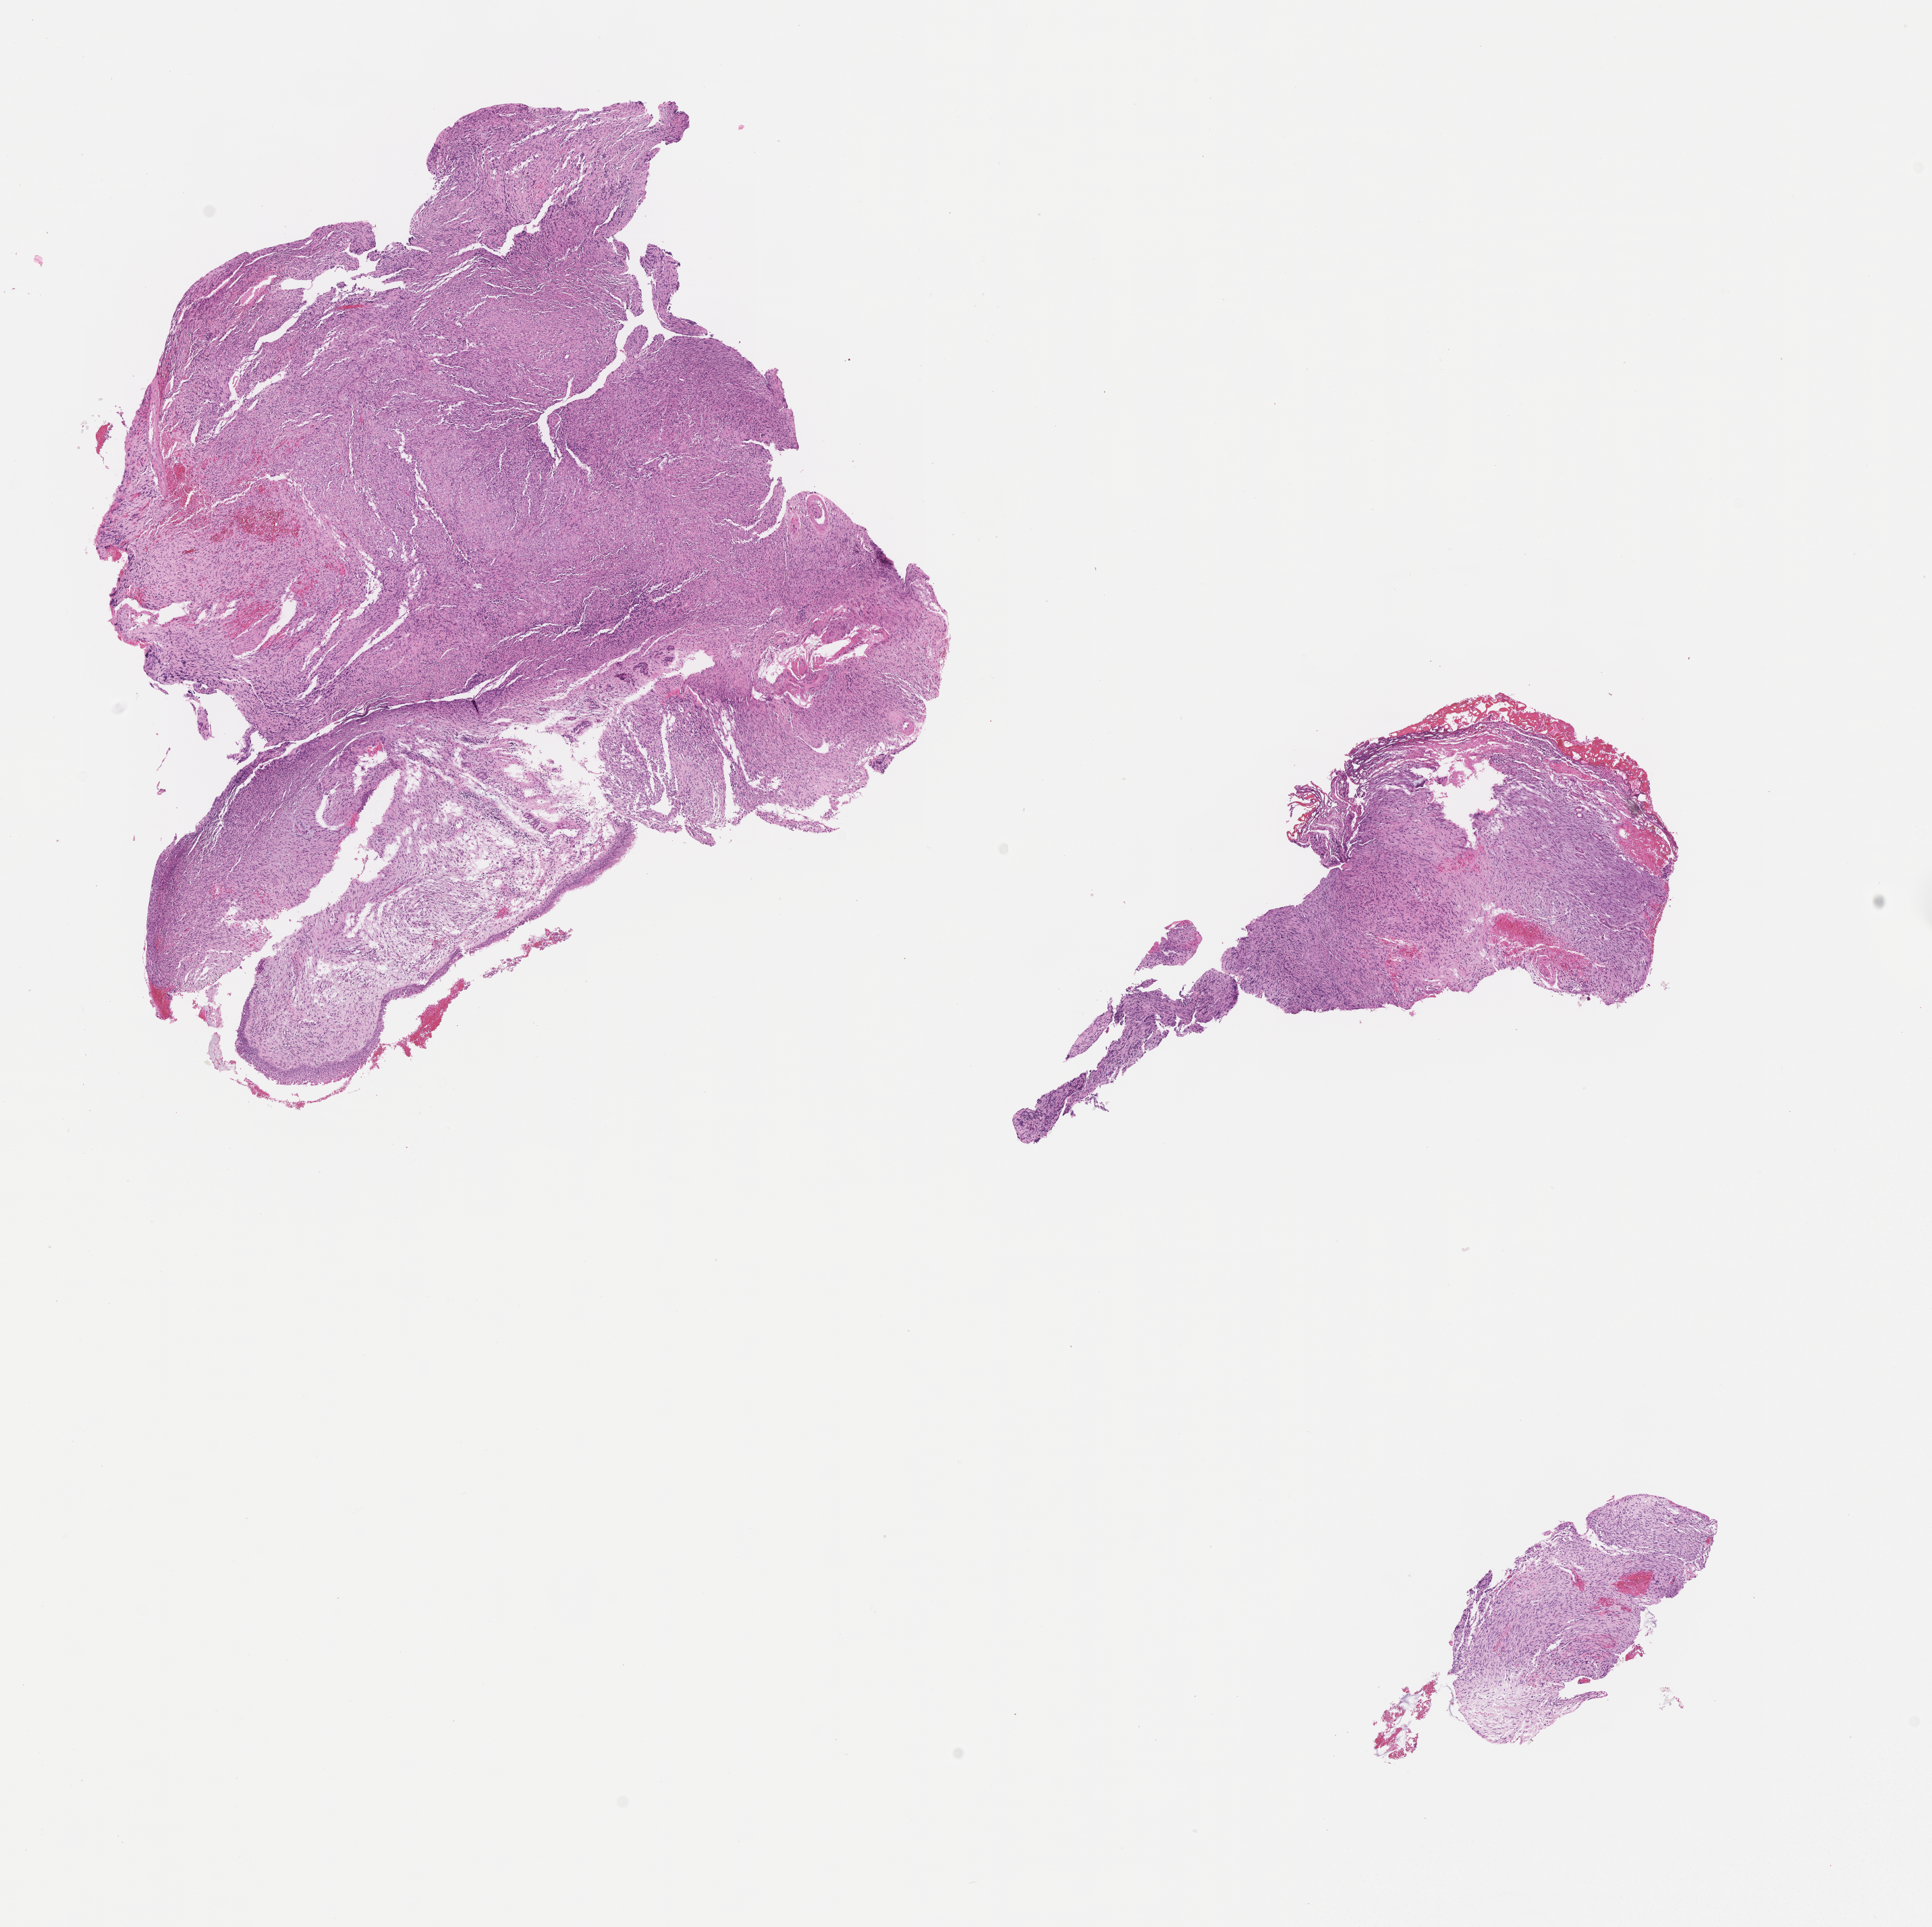
H&E whole-slide image of tumor tissue, low-resolution overview of the scanned area, about 11.6 x 11.5 mm, formalin-fixed, paraffin-embedded (FFPE) tissue, sample anatomic site: nasal cavity, right. Male patient, age at diagnosis 15.1 years.
Diagnosis: rhabdomyosarcoma; histological classification: spindle cell rhabdomyosarcoma.